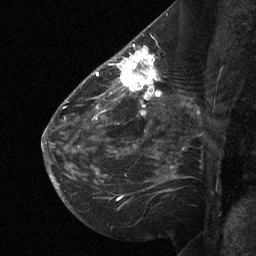
Breast MRI (dynamic contrast-enhanced), one sagittal slice; slice 37 of 64 in the series (ordered by position); dynamic contrast-enhanced study with each time point stored as its own series, time point 2 of 3 at this slice position (early post-contrast, ordered by acquisition time); 1.5 T; TE 4.8 ms, TR 27 ms; 2 mm slice thickness; 256 × 256 image matrix. Patient: female, 51 years. Case-level facts recorded for this patient, not image findings: setting: breast cancer imaged before/during neoadjuvant chemotherapy; receptor status: HR-positive, HER2-negative.
Structures marked on this image (semi-automatic segmentation, software-assisted and operator-edited):
- analysis volume of interest (the breast-tissue region the enhancement analysis was run in; not a lesion): bounding box (x1, y1, x2, y2) in pixels: (112, 46, 169, 106)
- tumour enhancement mask (voxels above the 90 % enhancement threshold inside the analysis volume of interest): (118, 47, 161, 100)